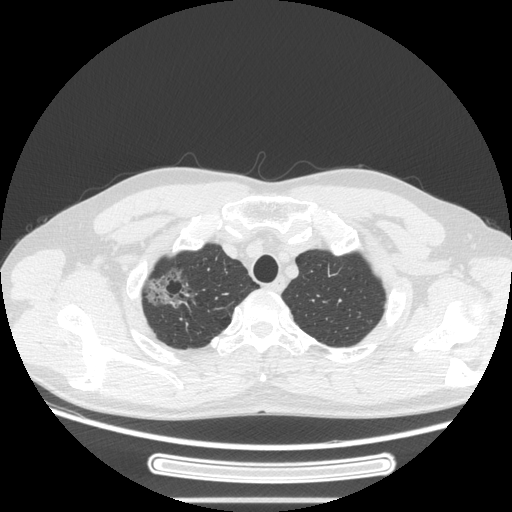
Chest CT, one axial slice; slice 229 of 269 in the series (ordered by position); lung window (W 1500 / L -600 HU); 1.25 mm slice thickness; 512 × 512 image matrix, field of view 382 × 382 mm. Patient: male, 53 years. Case-level facts recorded for this patient, not image findings: clinical TNM (as recorded): T1c N0 M0.
Structures marked on this image (bounding box drawn by a radiologist):
- lung tumour (recorded histology: adenocarcinoma): box from (x=142, y=262) to (x=193, y=314) px